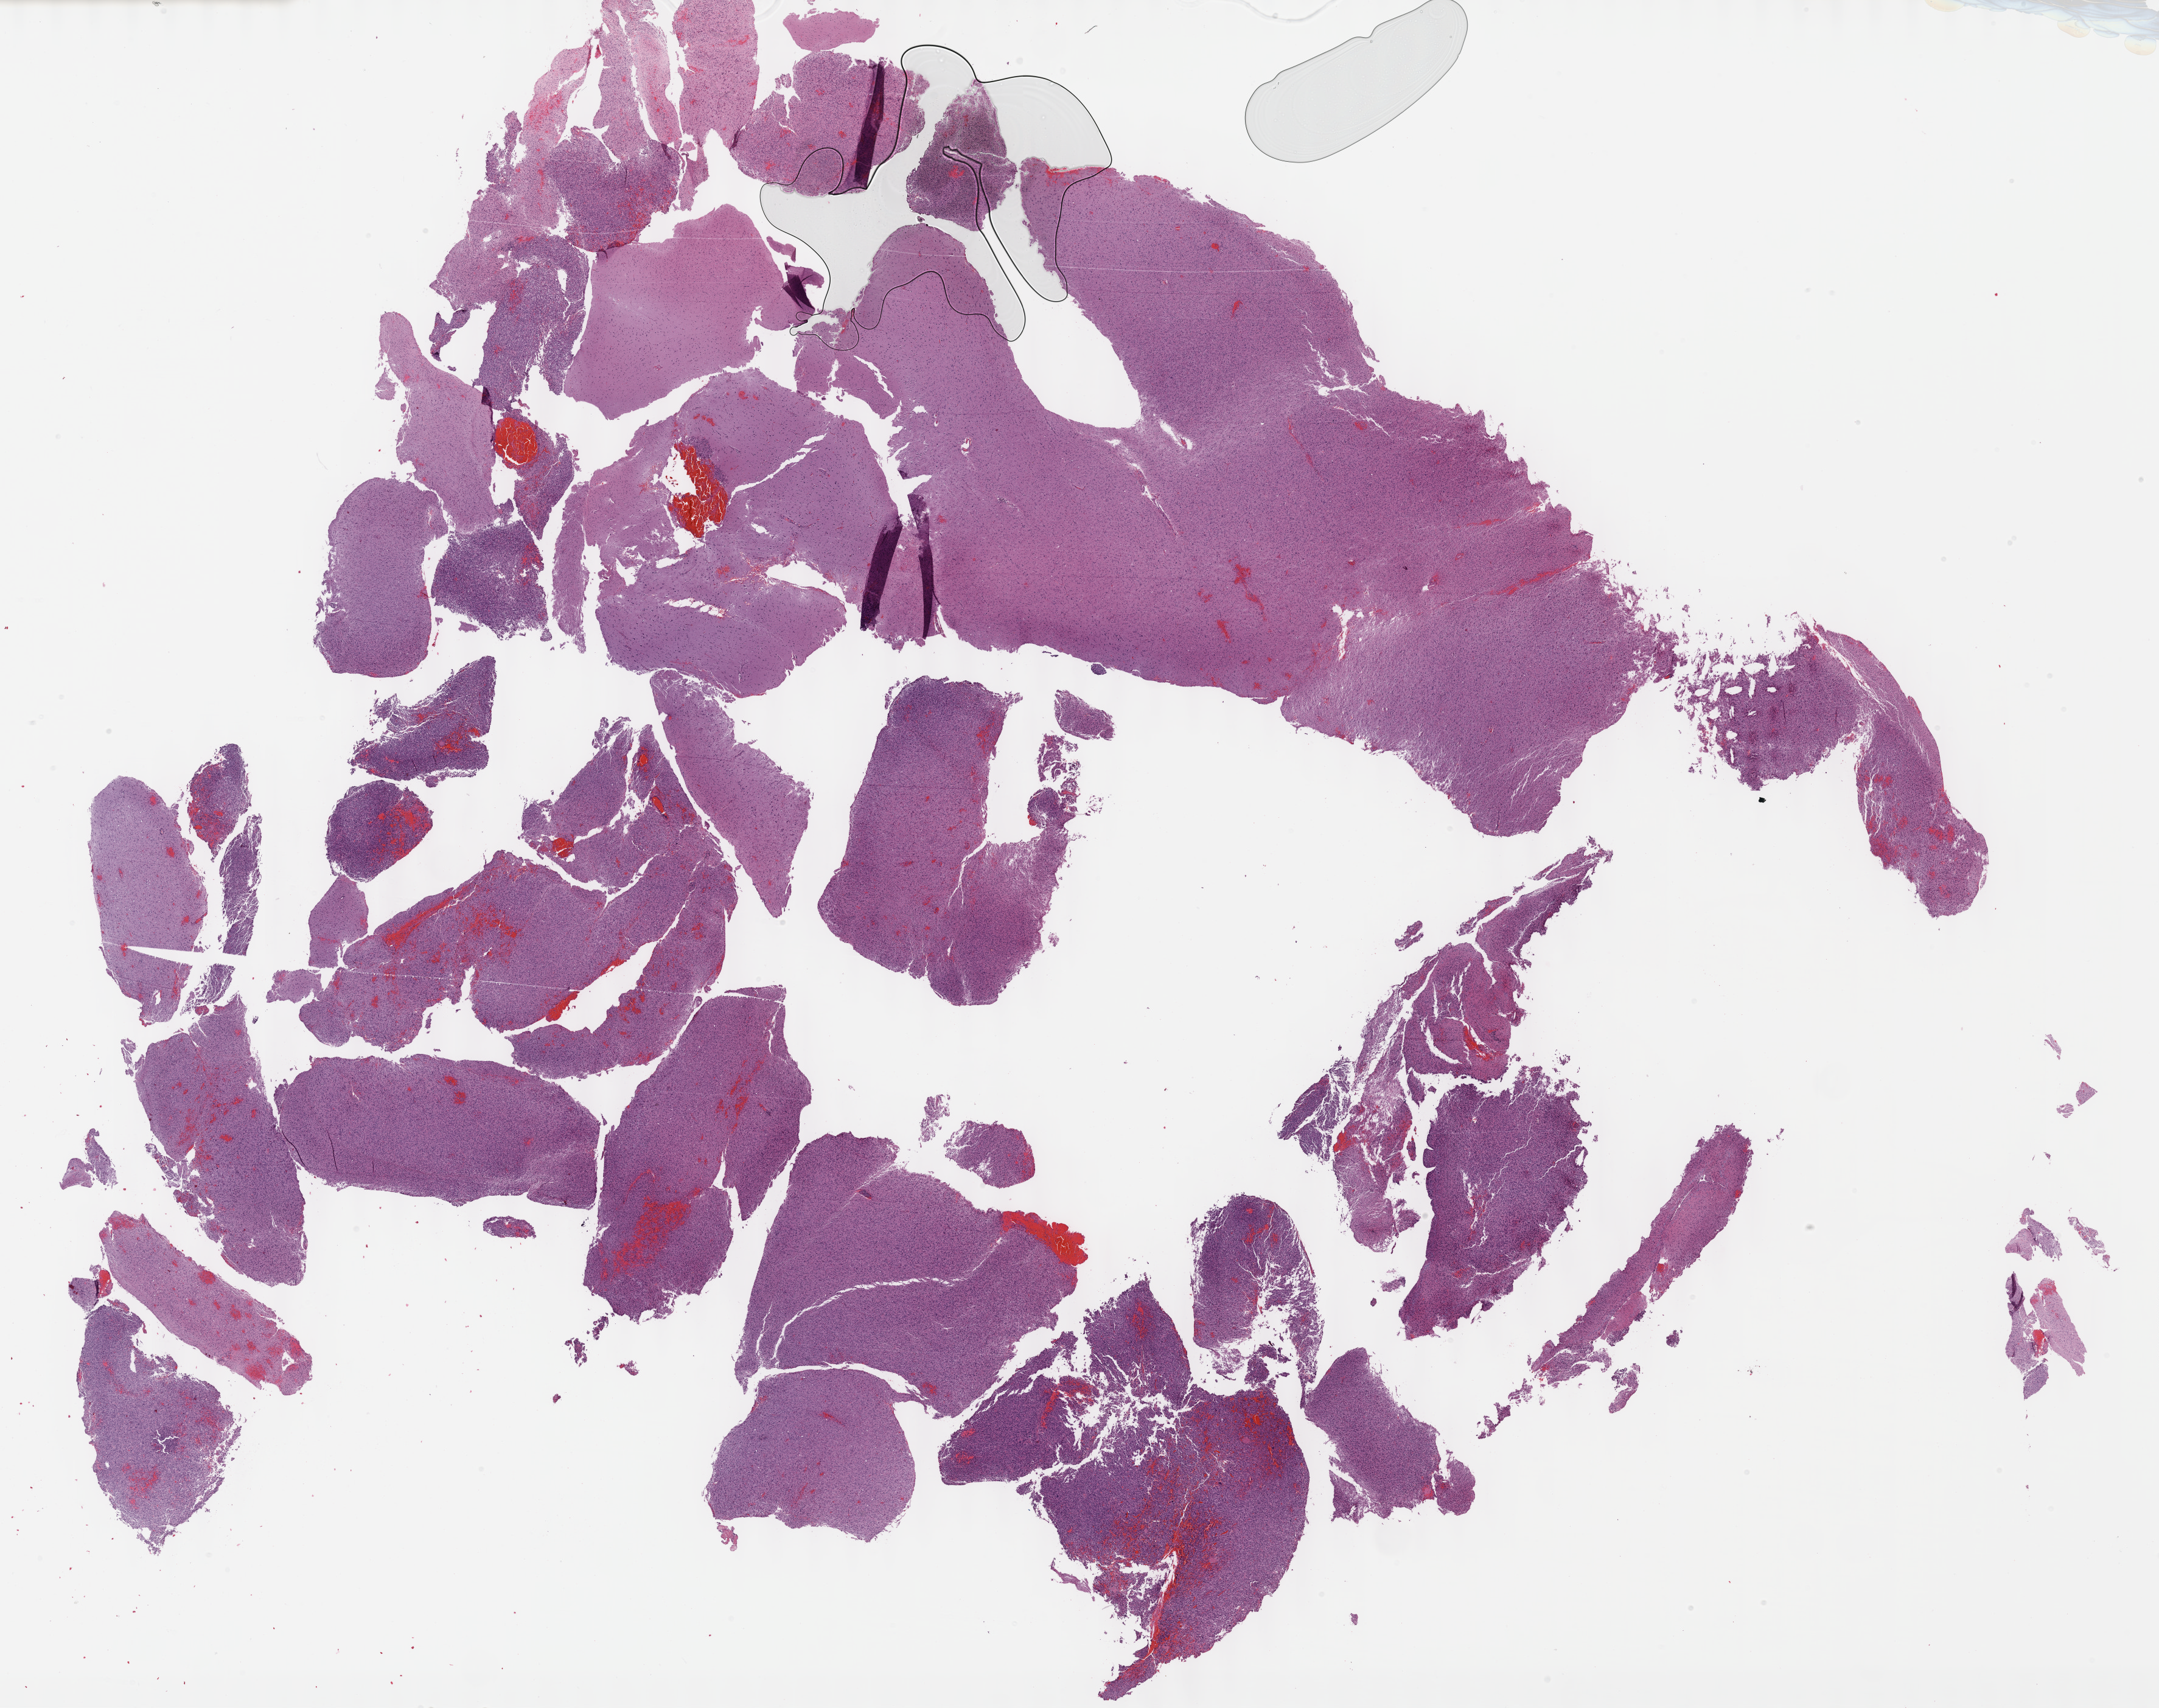
Hematoxylin and eosin (H&E) stained whole-slide image — low-resolution overview of the scanned area, about 28.7 x 22.7 mm (slide scanned at 40x). Formalin-fixed paraffin-embedded (FFPE) diagnostic section. Sample: primary tumour, brain. Female patient; age at initial diagnosis 55 years. Histologic grade: G3 (poorly differentiated).
* laterality: right
* pathologic diagnosis: Astrocytoma, anaplastic (cerebrum)